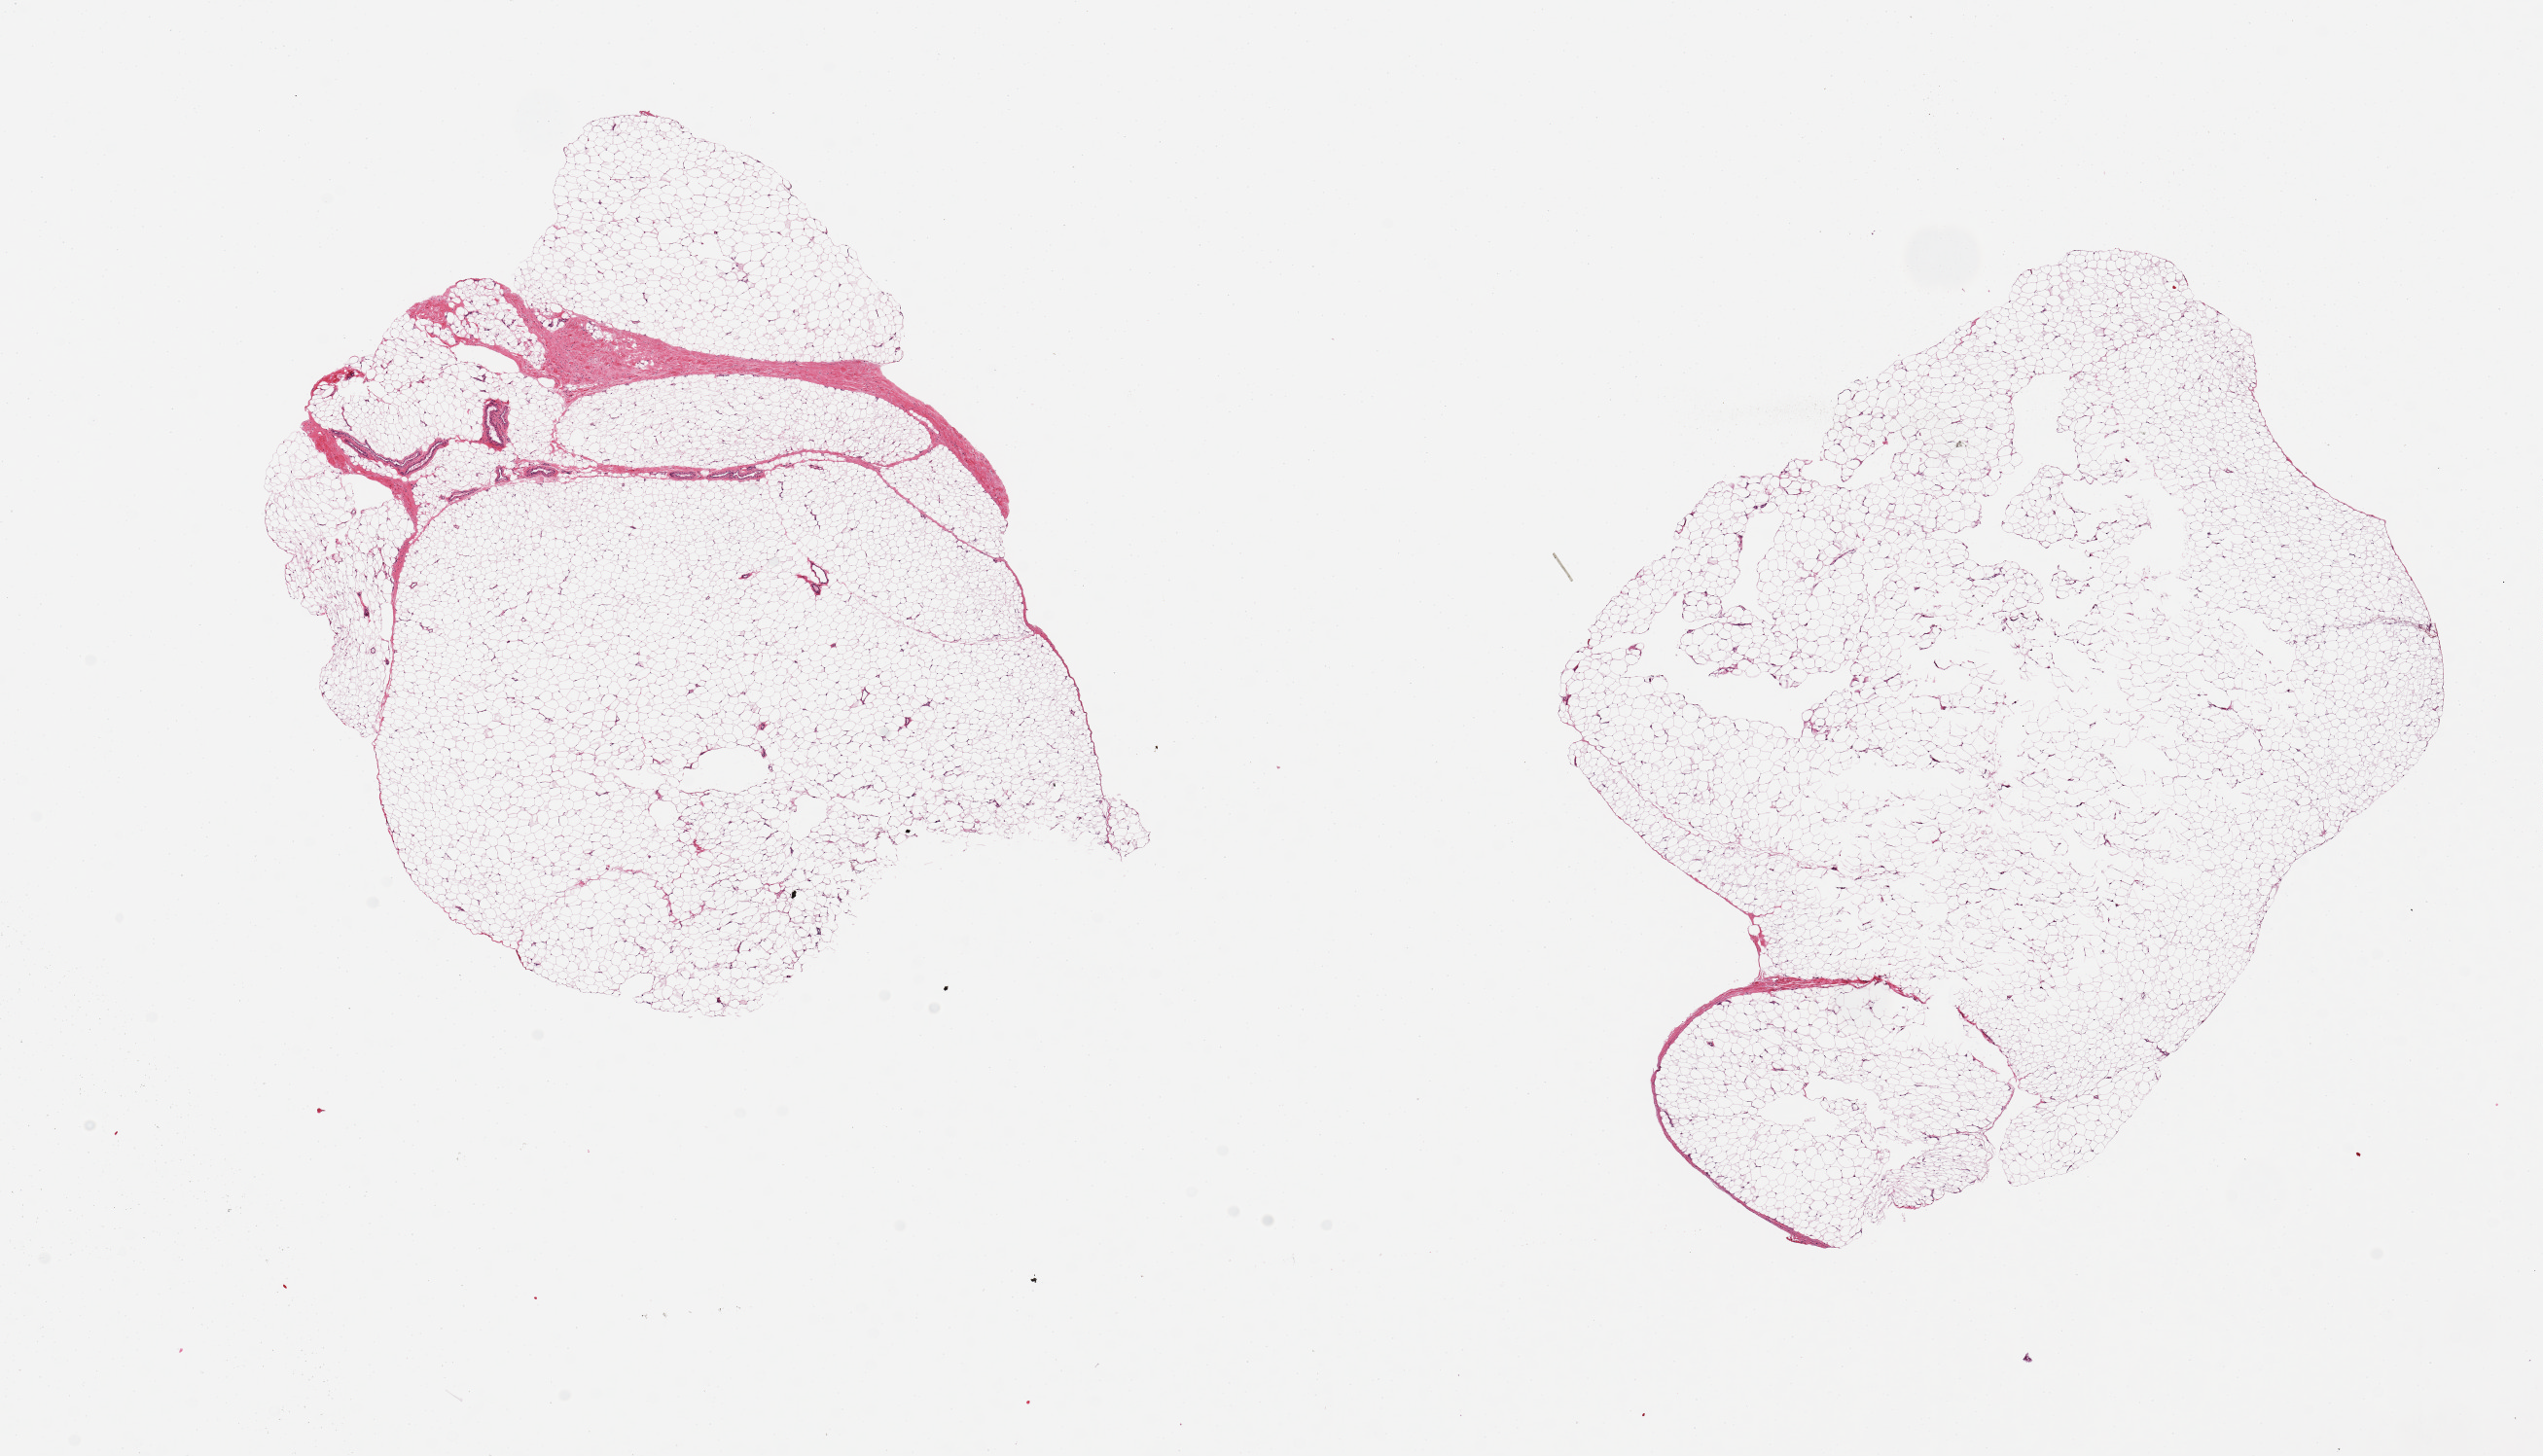
Whole-slide image, hematoxylin and eosin (H&E) stain, low-resolution overview of the scanned area, about 20.7 x 11.8 mm. PAXgene-fixed paraffin-embedded (PFPE) section. Target tissue: adipose tissue. Donor tissue sample. Male donor.
- reviewer comment on this tissue sample: 2 pieces 7x5 & 7x6 mm: well fixed